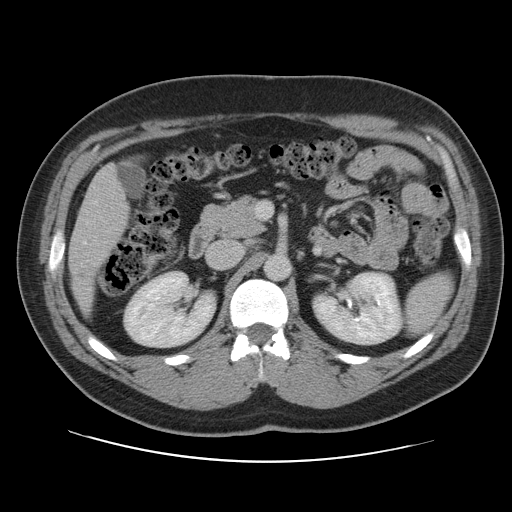
Contrast-enhanced abdominal CT, one axial slice; position 55 of 109 along the scan axis; intravenous contrast given; soft-tissue window (W 400 / L 40 HU); 5 mm slice thickness; 512 × 512 image matrix, field of view 402 × 402 mm. Male patient, age 35 years. From the clinical record (not read from this slice): diagnosis: colorectal cancer liver metastases, imaged before liver resection; multiple liver metastases: yes; largest metastasis: 2.8 cm; chemotherapy before resection: yes.
Structures marked on this image (expert manual segmentation):
- liver: bounding box (x1, y1, x2, y2) in pixels: (70, 167, 129, 316)
- planned liver remnant (the part of the liver to remain after resection): (70, 167, 129, 317)